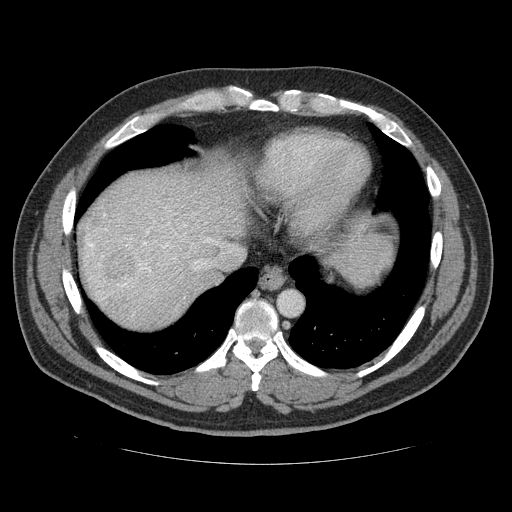
Contrast-enhanced abdominal CT (liver protocol), one axial slice. Reconstruction kernel STANDARD. Soft-tissue window (W 400 / L 40 HU). 2.5 mm slice thickness. 512 × 512 image matrix. Case-level facts recorded for this patient, not image findings: diagnosis: hepatocellular carcinoma (patient treated with transarterial chemoembolisation; whether this scan precedes or follows treatment is not stated here); TNM stage (as recorded): Stage-II; Child-Pugh class: B; tumour differentiation: moderately differentiated; tumour nodularity: multinodular.
Structures marked on this image (semi-automatically segmented with operator editing):
- abdominal aorta: box from (x=279, y=292) to (x=302, y=315) px
- liver parenchyma outside the tumour (the mass and vessels are separate outlines, so this box may not span the whole liver): (x=80, y=170)–(x=248, y=322)
- mass: (x=96, y=247)–(x=140, y=286)
- liver vessels: (x=86, y=213)–(x=155, y=273)